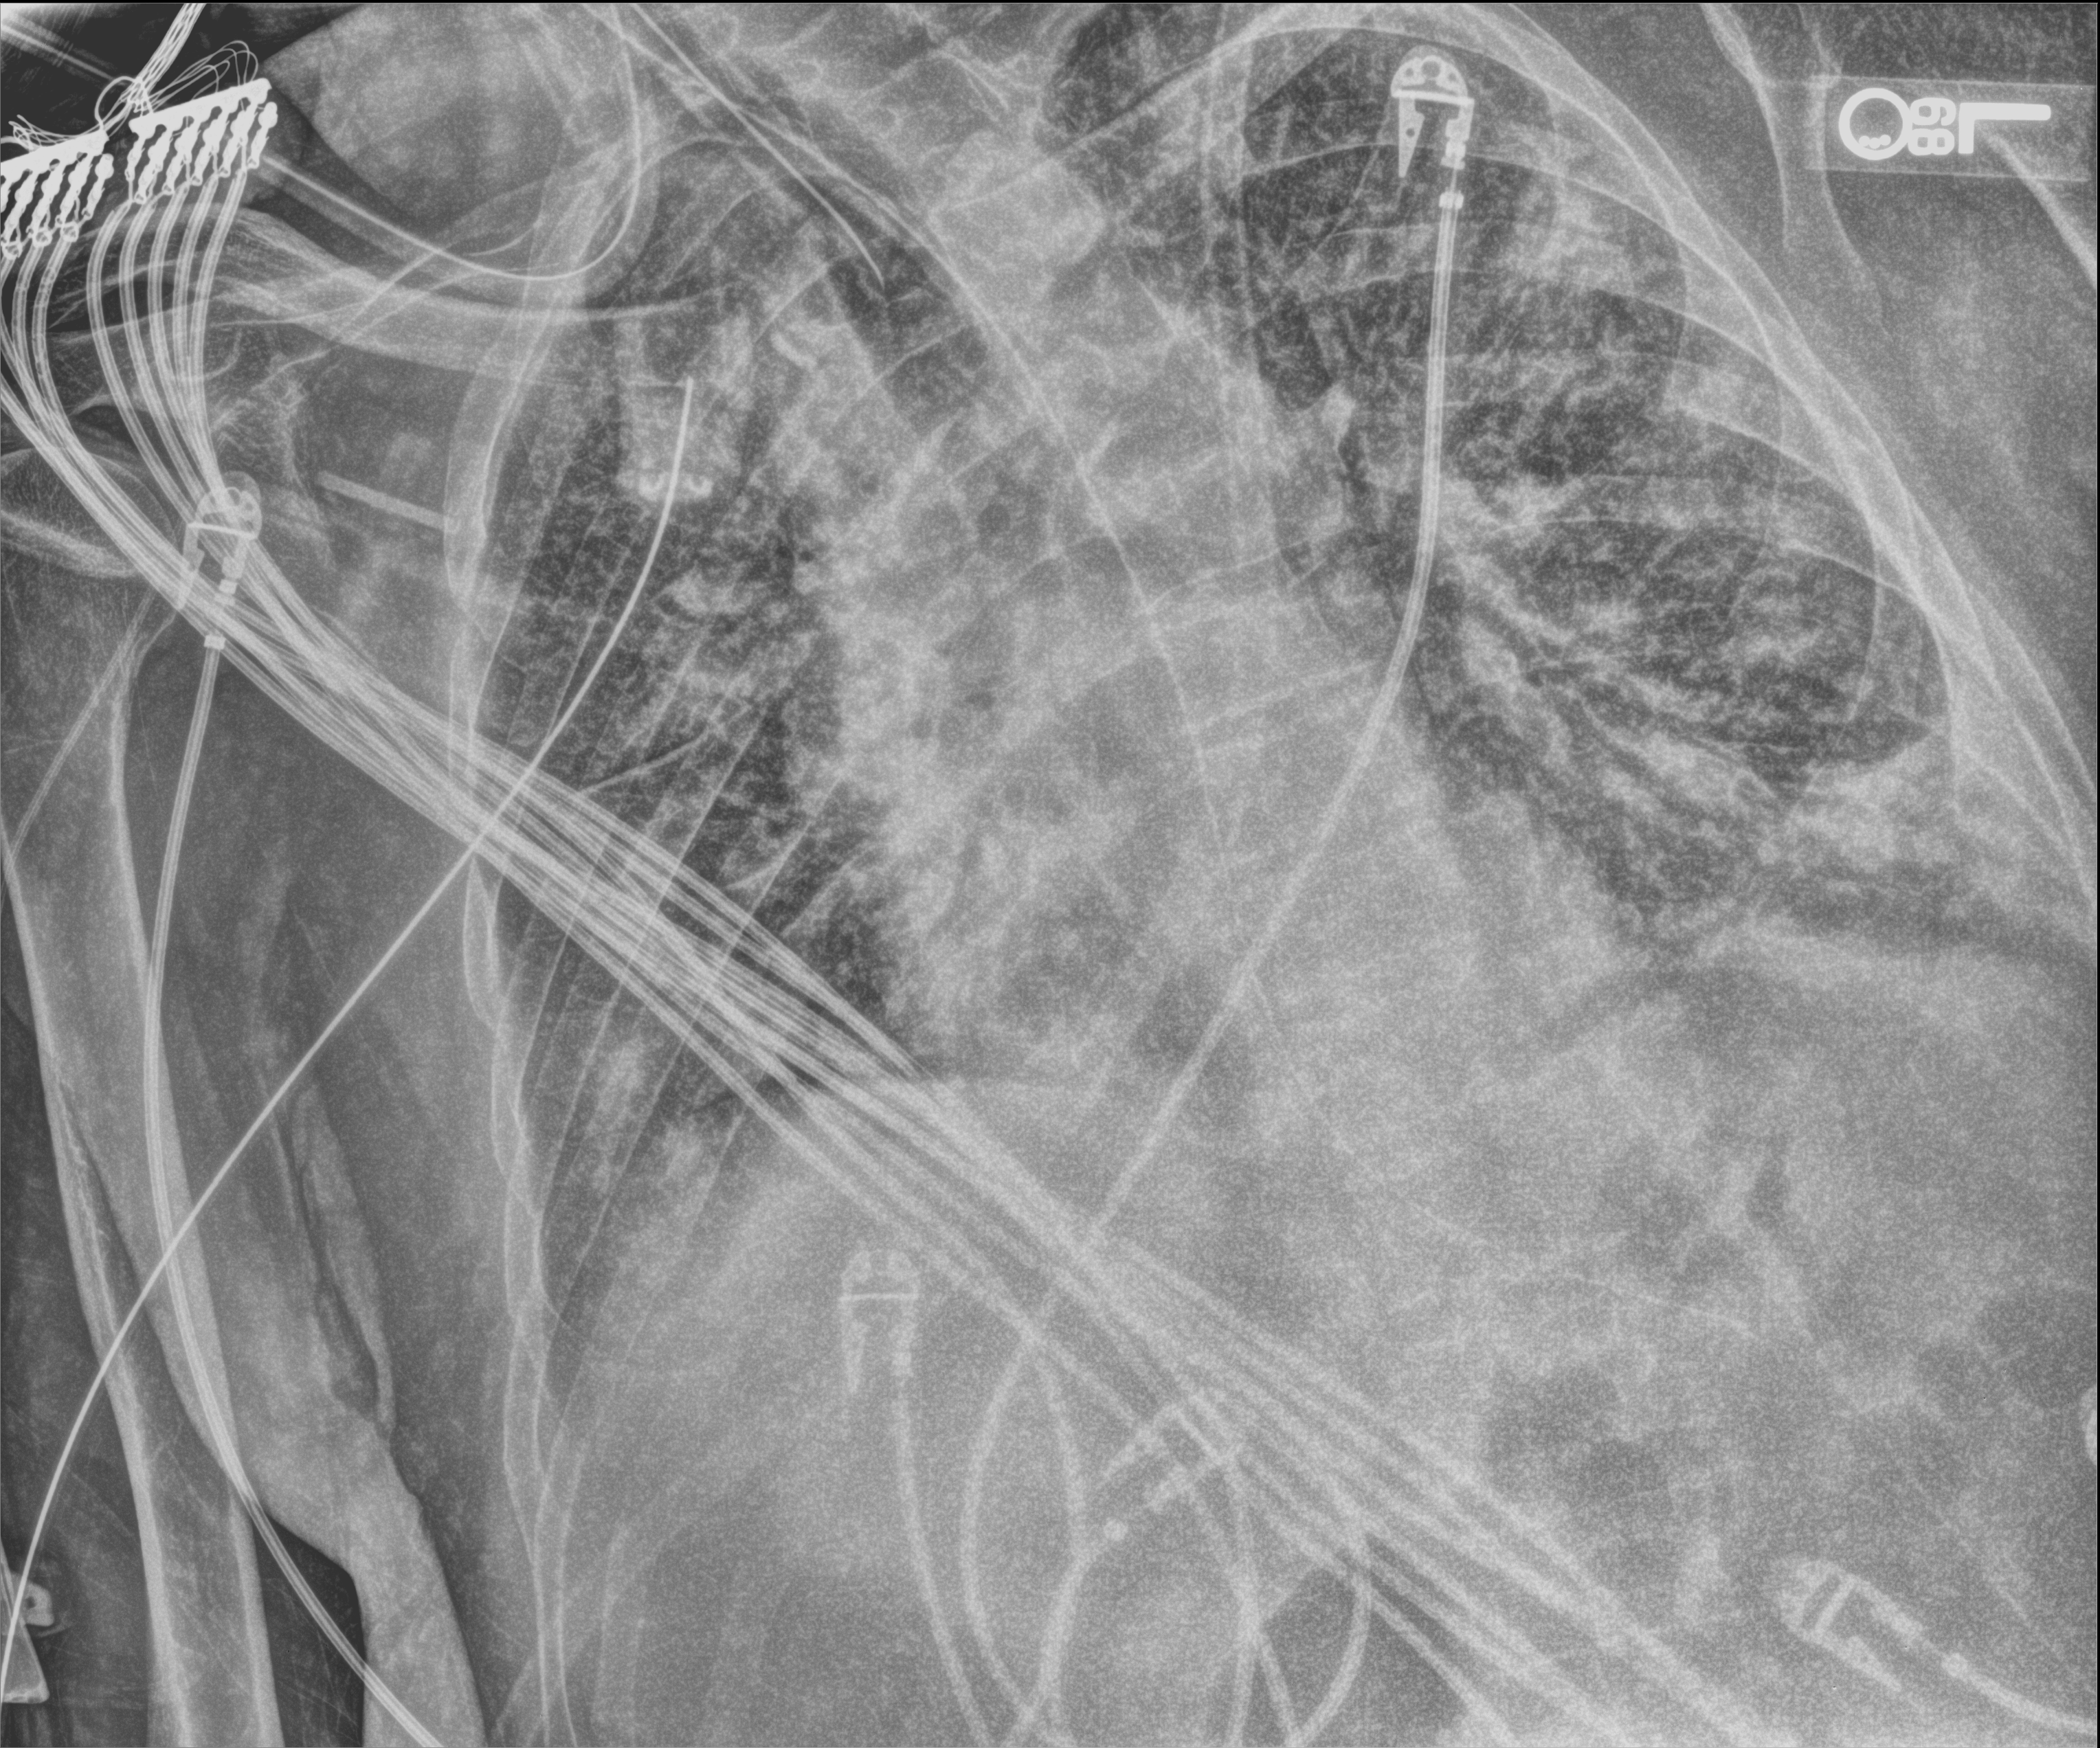
Bedside chest radiograph (computed radiography); anteroposterior (AP) projection. Male patient hospitalised with COVID-19, age 60–74 years.
Admission-level facts for this patient (not findings on this image; timing relative to this image not recorded):
- hypertension (admission record): no